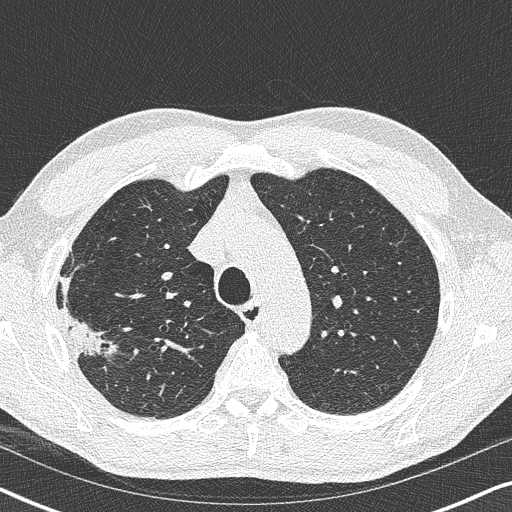
Low-dose screening chest CT, one axial slice; reconstruction kernel B50f; 120 kVp; lung window (W 1500 / L -600 HU); 512 × 512 image matrix.
Outlined on this slice (outlined manually by an expert reader):
- lesion 1 (tumor, upper lobe of right lung): bounding box <60,307,117,356> (left, top, right, bottom; pixels)